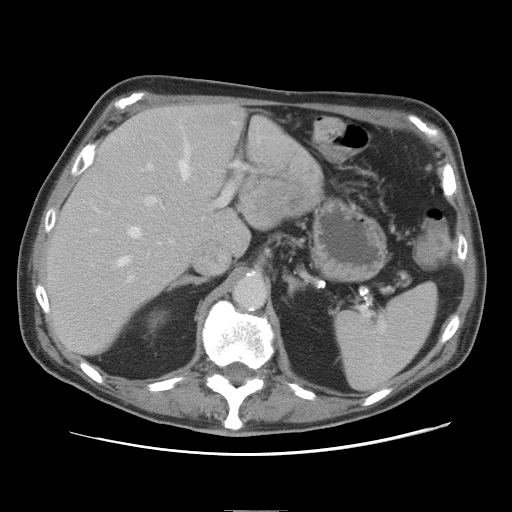
Contrast-enhanced abdominal CT, one axial slice; position 51 of 89 along the scan axis; 120 kVp; intravenous contrast given; soft-tissue window (W 400 / L 40 HU); 5 mm slice thickness; 512 × 512 image matrix, field of view 375 × 375 mm. Male patient, age 69 years. Case-level facts recorded for this patient, not image findings: diagnosis: colorectal cancer liver metastases, imaged before liver resection; multiple liver metastases: no; largest metastasis: 8.5 cm.
Structures marked on this image (manually delineated by an expert):
- hepatic veins: bounding box [x1, y1, x2, y2] px = [118, 139, 192, 266]
- liver: [48, 105, 324, 354]
- planned liver remnant (the part of the liver to remain after resection): [48, 105, 246, 354]
- portal vein (with intrahepatic branches): [127, 141, 260, 284]
- liver metastasis: [285, 193, 303, 209]